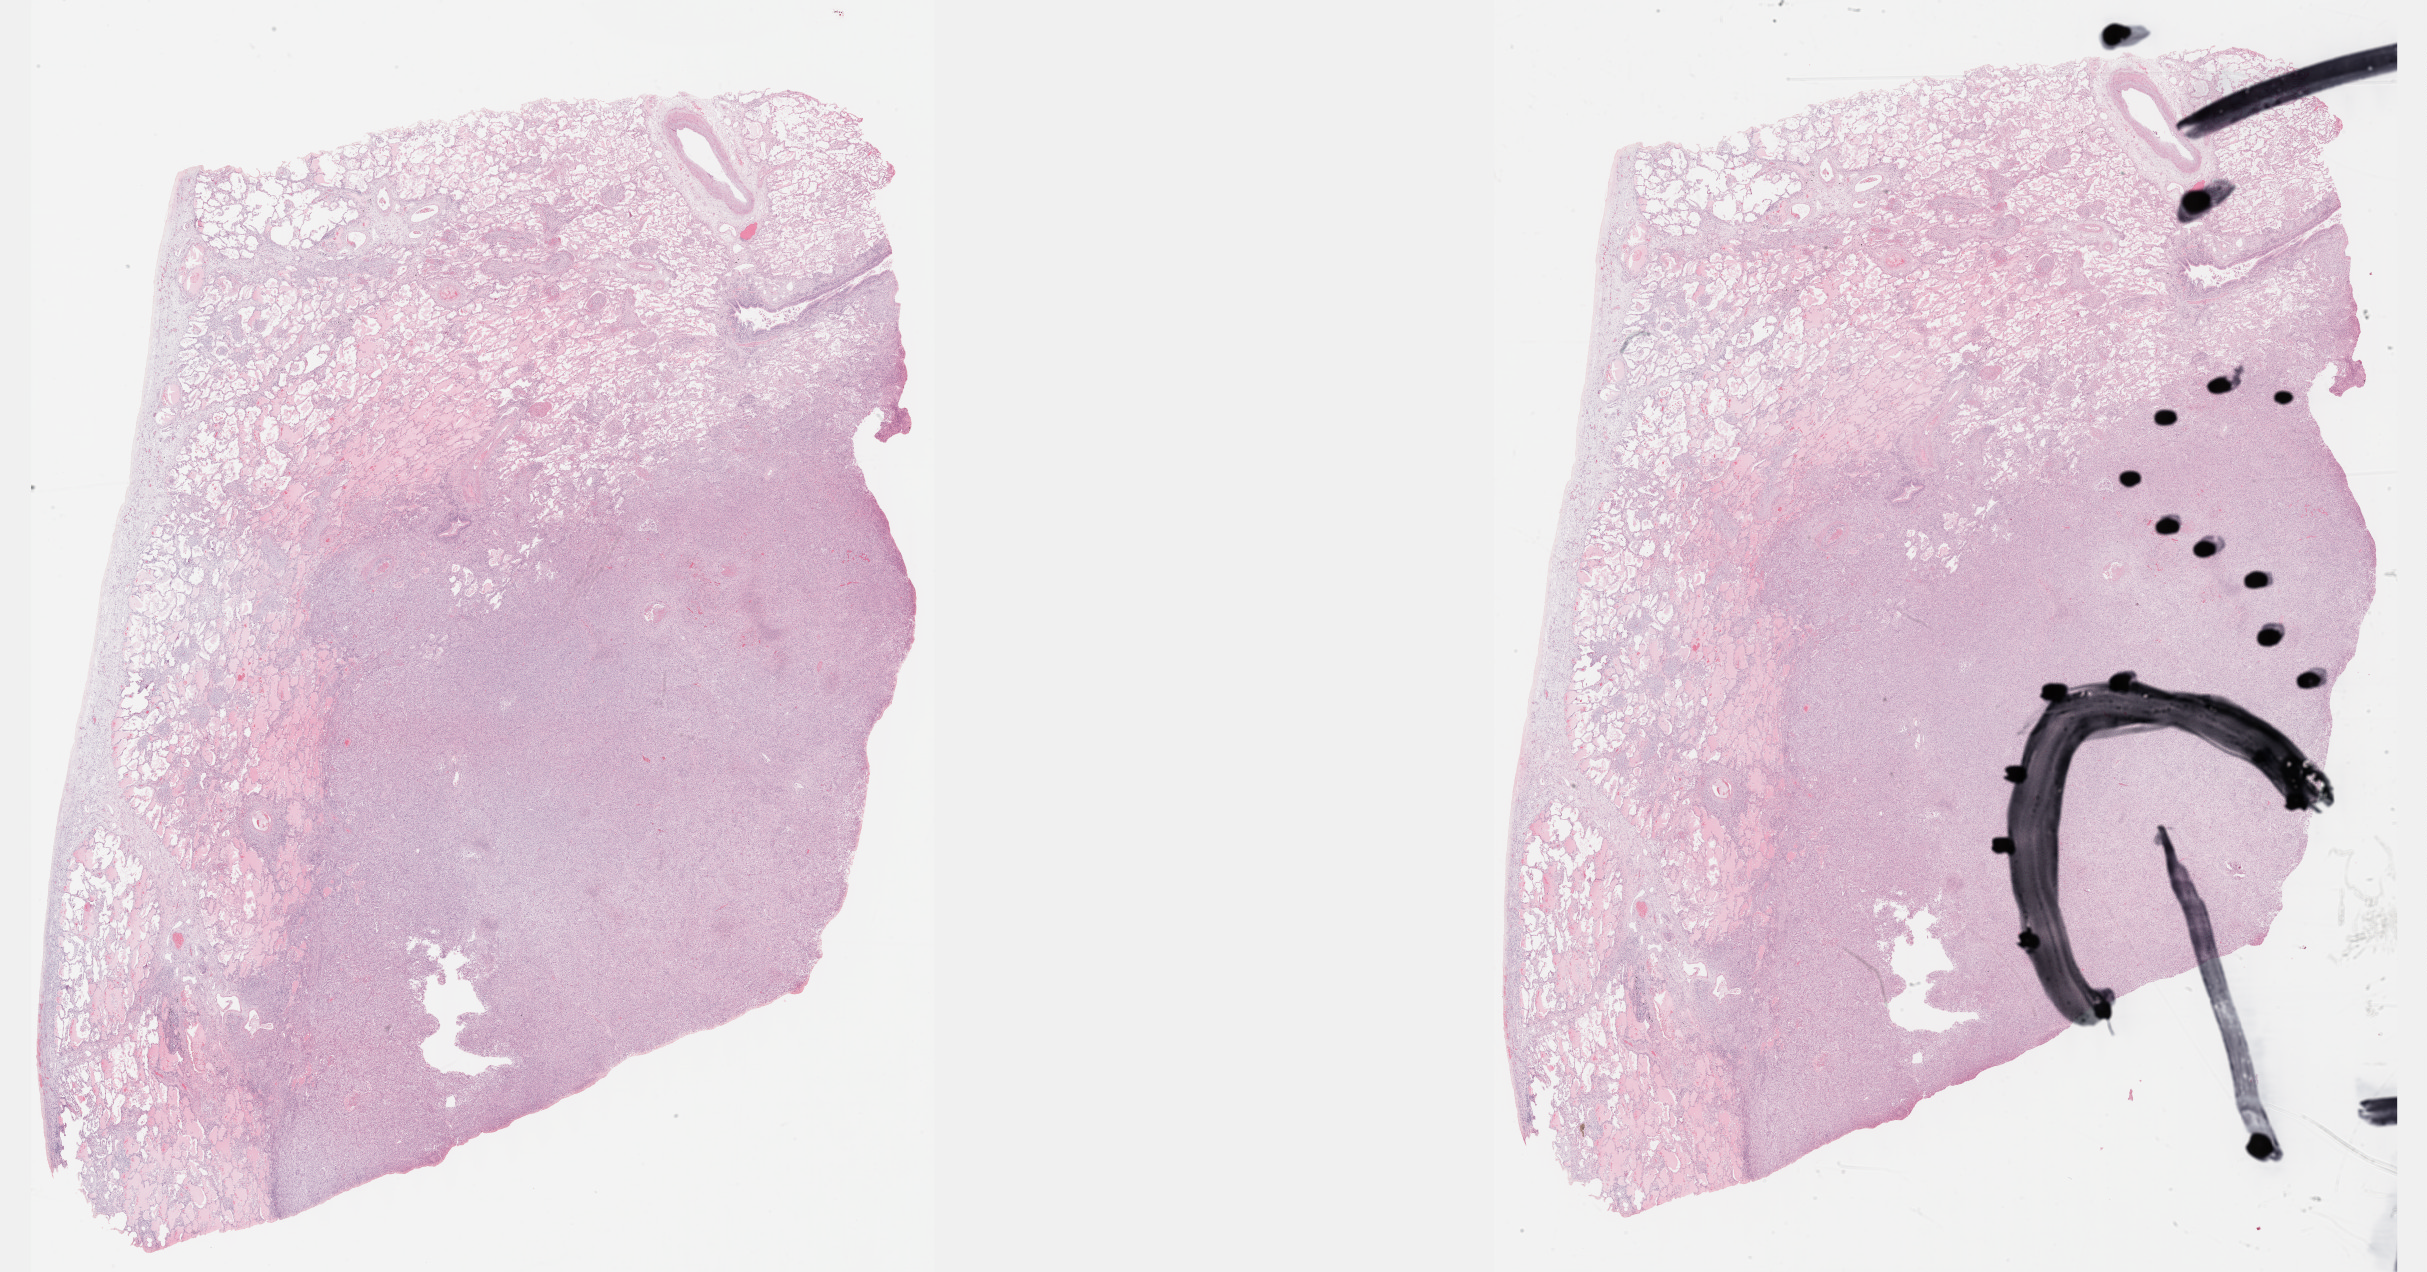
Whole-slide histology image, H&E-stained, whole scanned area (about 39.2 x 20.6 mm, slide scanned at 40x) shown as a low-resolution overview; formalin-fixed paraffin-embedded (FFPE) diagnostic section; primary tumour sample from the lung. Female patient; age at initial diagnosis 72 years.
Laterality: right. AJCC pathologic stage: IIIB. Histologic diagnosis: Adenocarcinoma, NOS (lower lobe, lung).